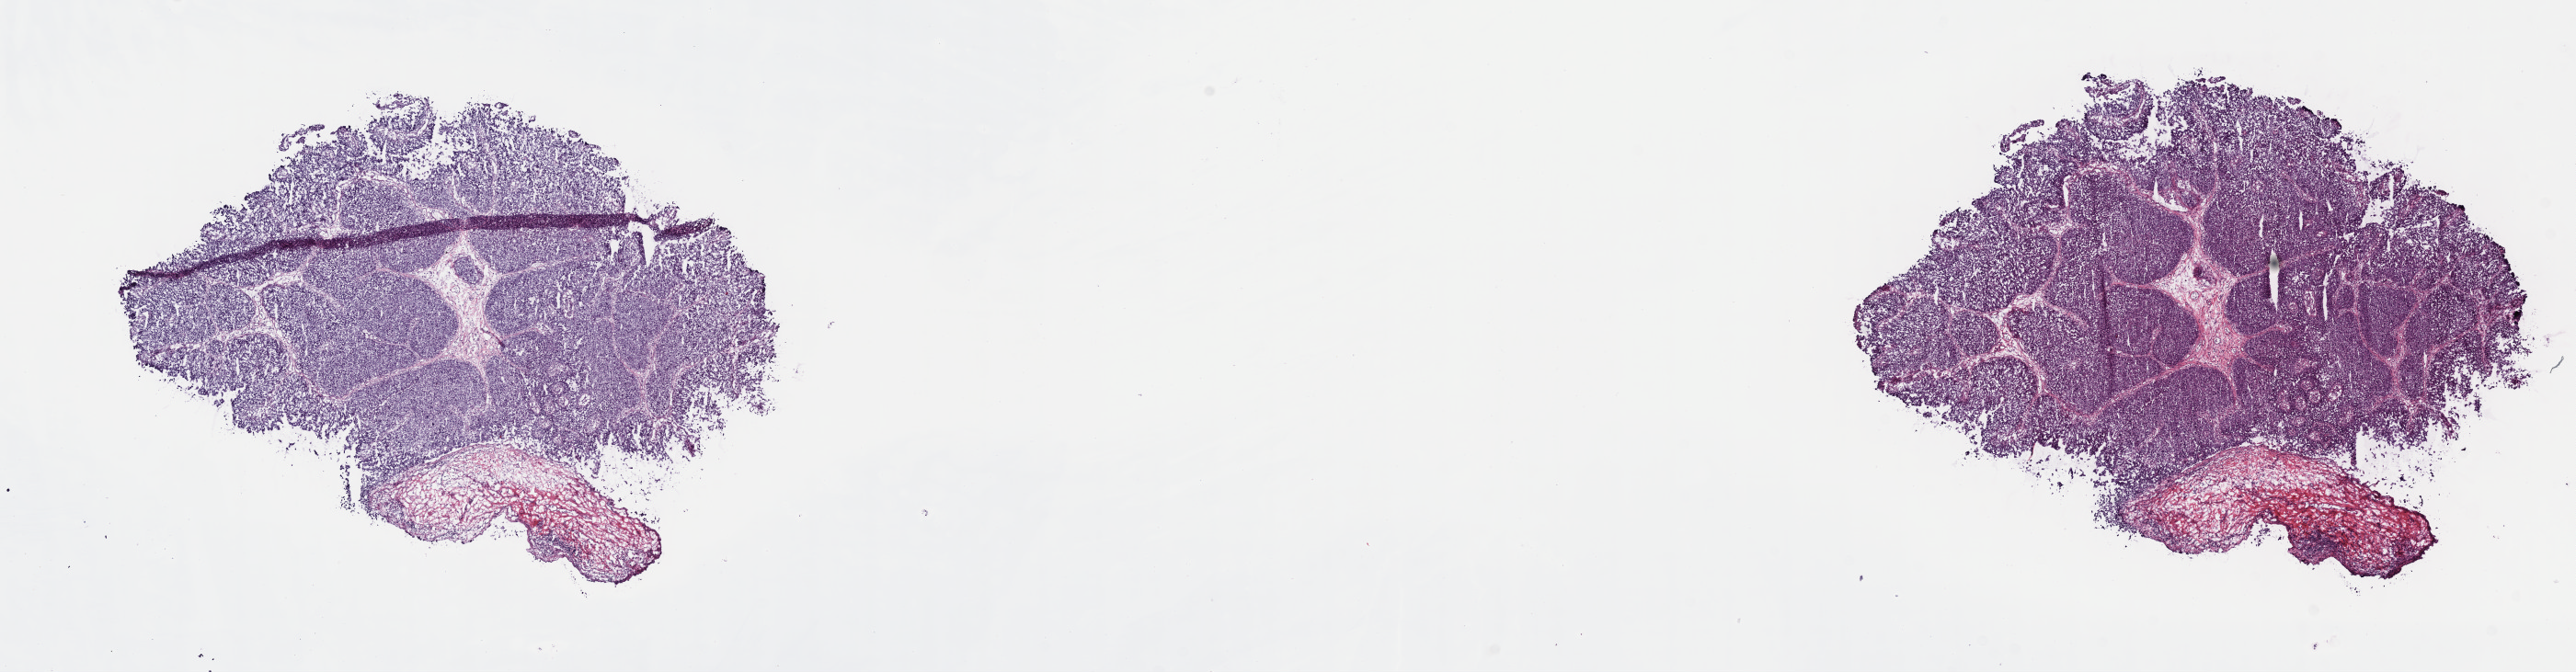
Digitized H&E tissue section (whole slide) — shown as a low-resolution overview of the whole scanned area (about 22.7 x 5.9 mm, from a 40x scan), frozen section, bladder, primary tumour sample. Patient: male, age at initial diagnosis 66 years. Histologic grade: high grade. Composition of this section per pathologist review: tumour cells 90%, tumour nuclei 75%, normal cells 10%, stromal cells 0%, necrosis 0%. Infiltration values recorded for this section: lymphocyte infiltration 3%, monocyte infiltration 0%, neutrophil infiltration 0%.
AJCC pathologic stage: IV (7th edition). TNM: T3a N2 MX. Histologic diagnosis: Transitional cell carcinoma (lateral wall of bladder).